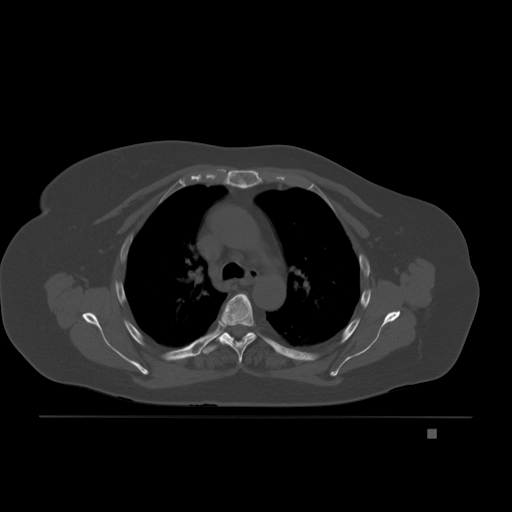
CT including the spine, one axial slice; slice 150 of 221 in the series (ordered by position); bone window (W 1800 / L 400 HU); 3 mm slice thickness; 512 × 512 image matrix, field of view 474 × 474 mm. Female patient, age 63 years. Case-level facts recorded for this patient, not image findings: primary cancer: breast.
Structures marked on this image (semi-automatic segmentation, software-assisted and operator-edited):
- T4 vertebra: bounding box <217,293,256,363> (left, top, right, bottom; pixels)
- T5 vertebra: <203,331,270,355>